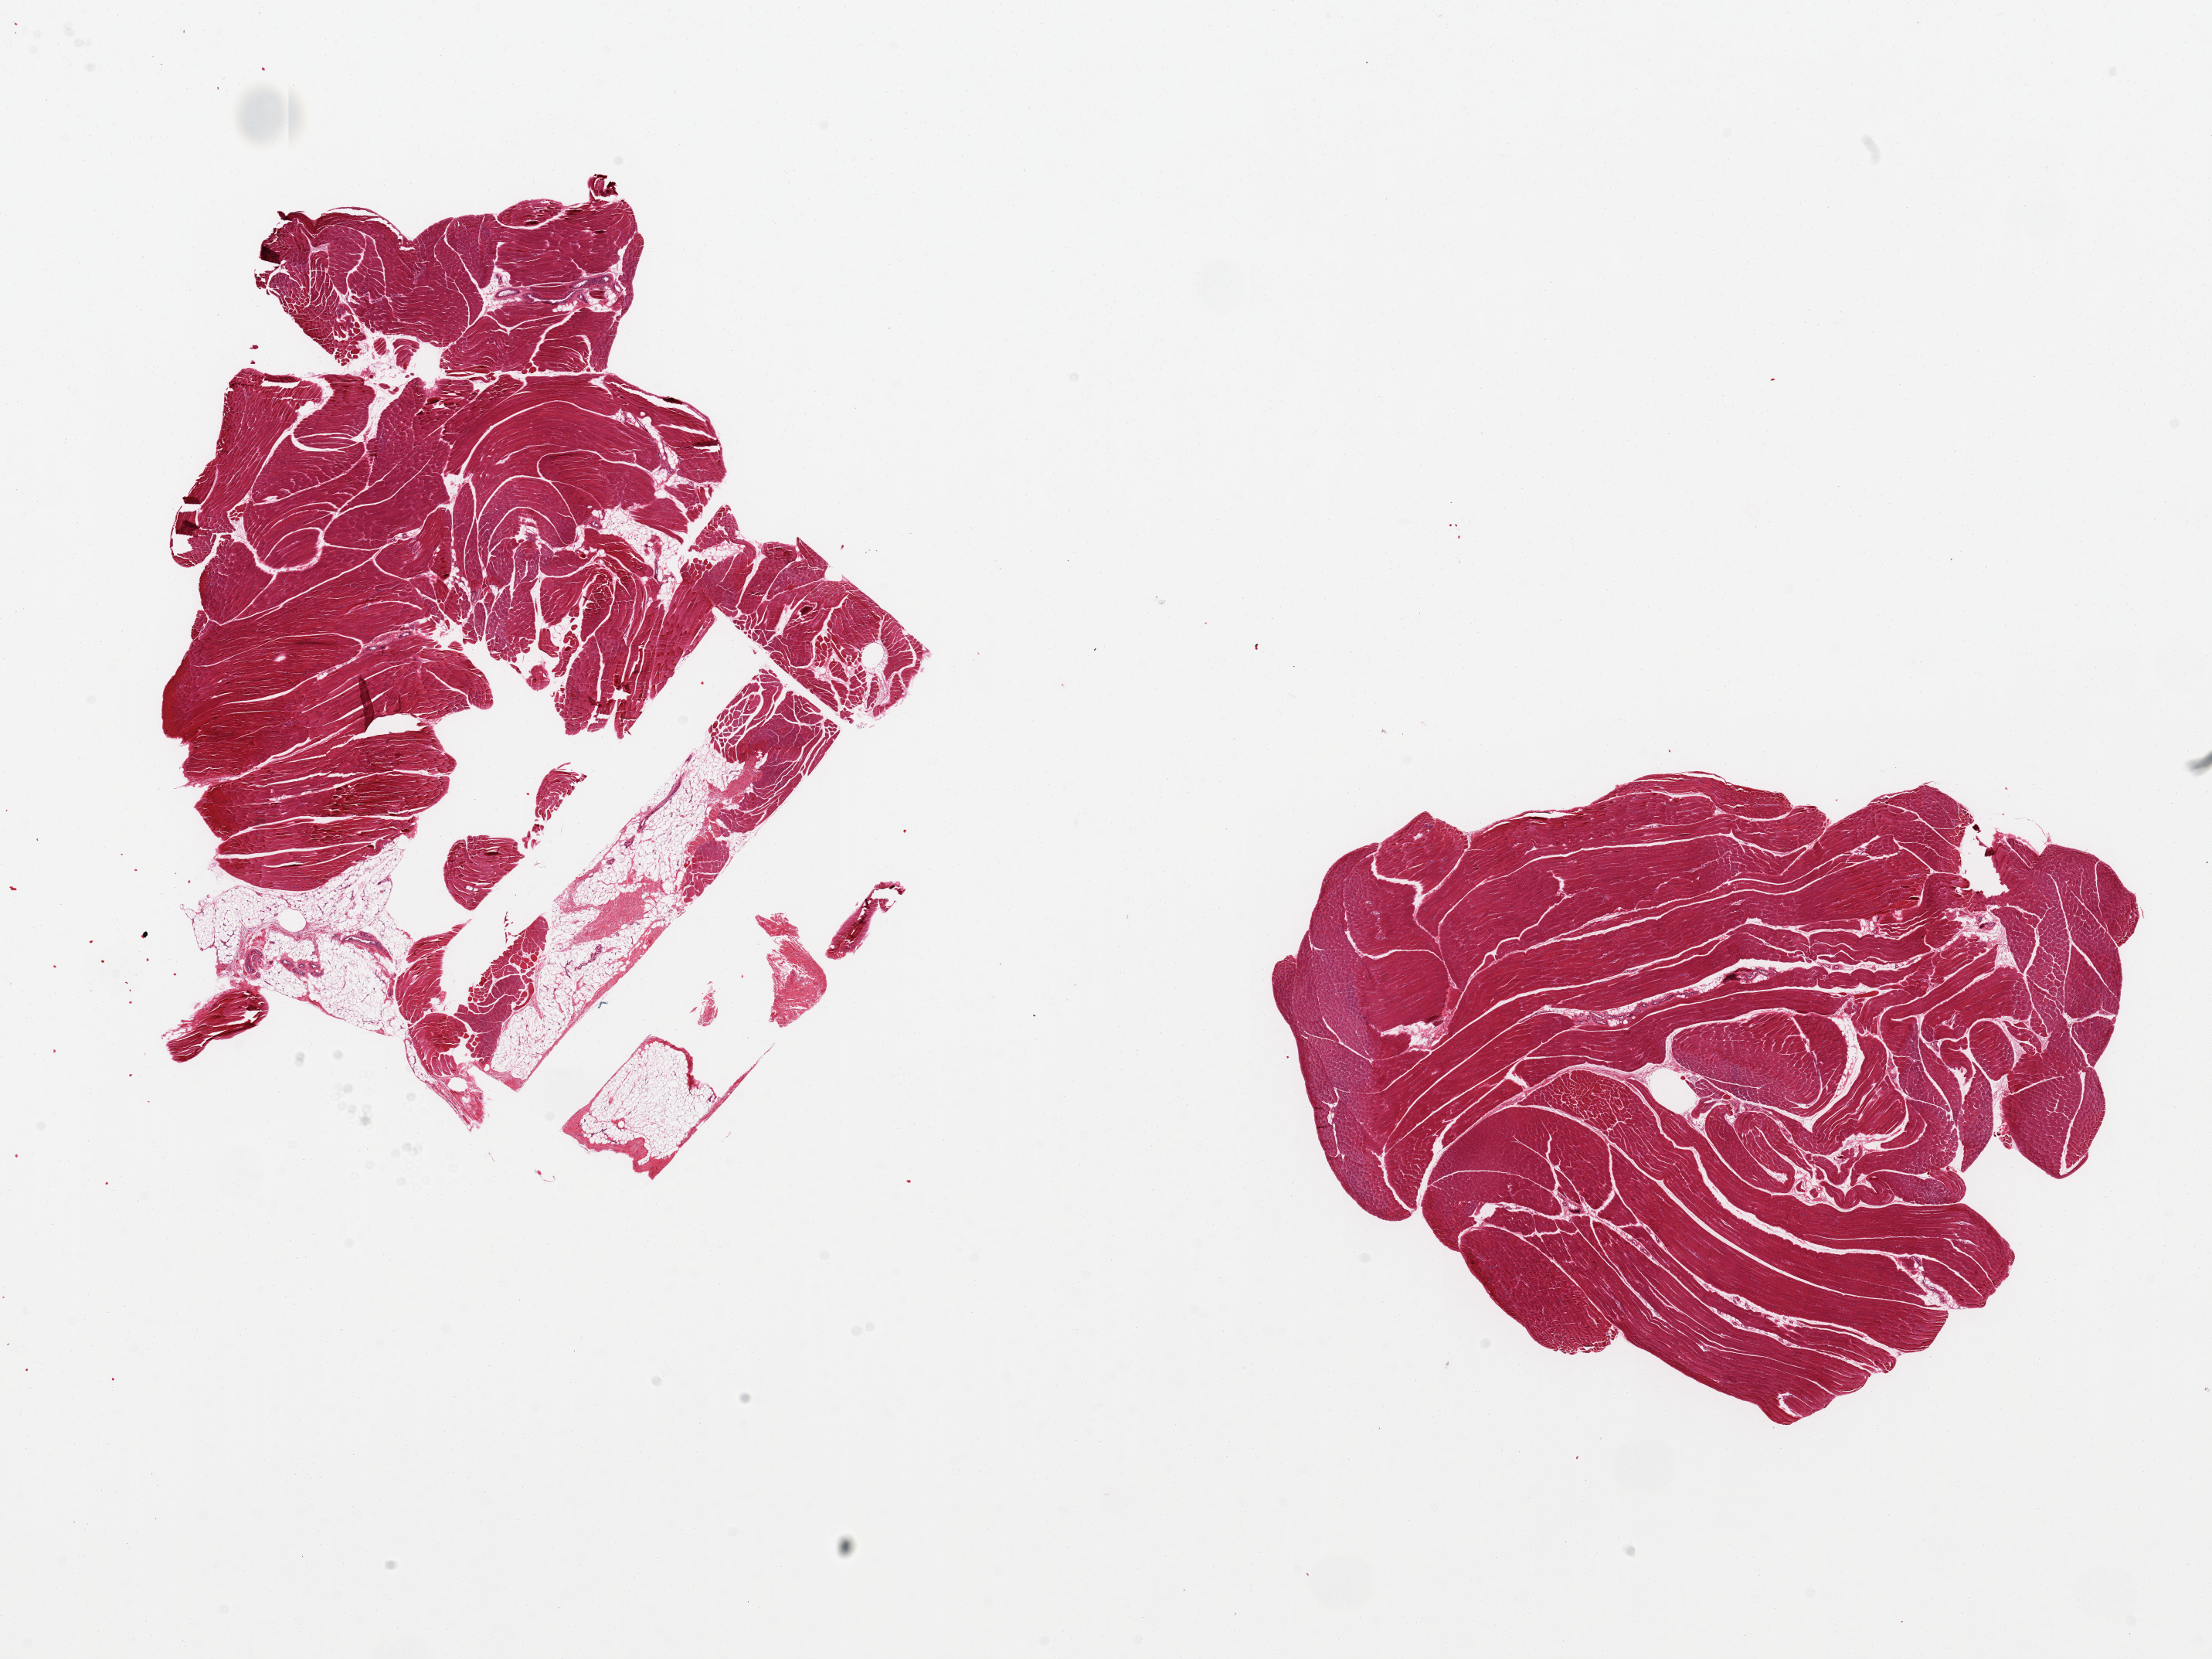
Whole-slide image, hematoxylin and eosin (H&E) stain, shown as a low-resolution overview of the whole scanned area (about 22.6 x 17.0 mm). PAXgene-fixed paraffin-embedded (PFPE) section. Sampled site (target tissue): skeletal muscle. Tissue donor sample. Donor sex: female.
Reviewer comment on this tissue sample: 2 pieces, one piece is fragmented, ~10-20% fat and portion of tendon.